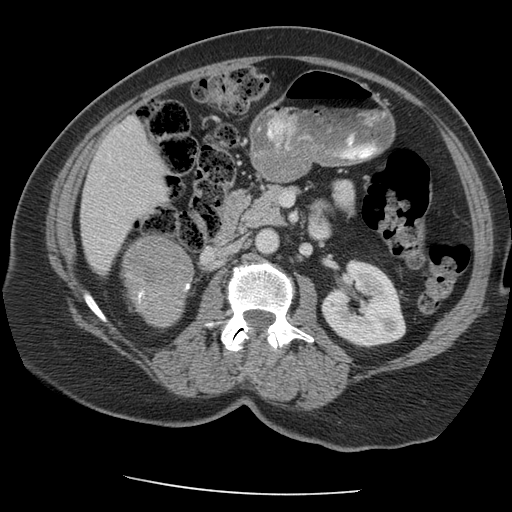
Contrast-enhanced abdominal CT, one axial slice; slice 108 of 163 in the series (ordered by position); reconstruction kernel STANDARD; 140 kVp; intravenous contrast given; soft-tissue window (W 400 / L 40 HU); 512 × 512 image matrix, field of view 360 × 360 mm. Female patient, age 70 years. From the clinical record (not read from this slice): diagnosis: adrenocortical carcinoma; tumour side: right adrenal; tumour size at pathology: 9.5 cm; Ki-67 index: 5 %; stage (as recorded): 2.
Annotated regions visible in this slice (semi-automatically segmented with operator editing):
- mass: bounding box [x1, y1, x2, y2] px = [123, 237, 190, 325]